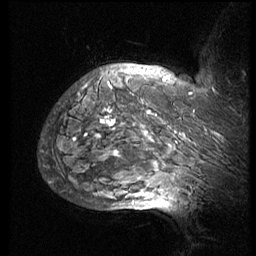
Breast MRI (dynamic contrast-enhanced), one sagittal slice. Position 59 of 74 along the scan axis. 3 images stored at this slice position (order not interpretable as contrast timing). 1.5 T. TE 4.2 ms, TR 8.9 ms. 256 × 256 image matrix, field of view 200 × 200 mm. Female patient, age 57 years. Case-level facts recorded for this patient, not image findings: setting: breast cancer imaged before/during neoadjuvant chemotherapy; receptor status: HER2-positive.
Annotated regions visible in this slice (semi-automatically segmented with operator editing):
- analysis volume of interest (the breast-tissue region the enhancement analysis was run in; not a lesion): bounding box (x1, y1, x2, y2) in pixels: (51, 67, 248, 173)
- tumour enhancement mask (voxels above the 140 % enhancement threshold inside the analysis volume of interest): (73, 78, 213, 155)